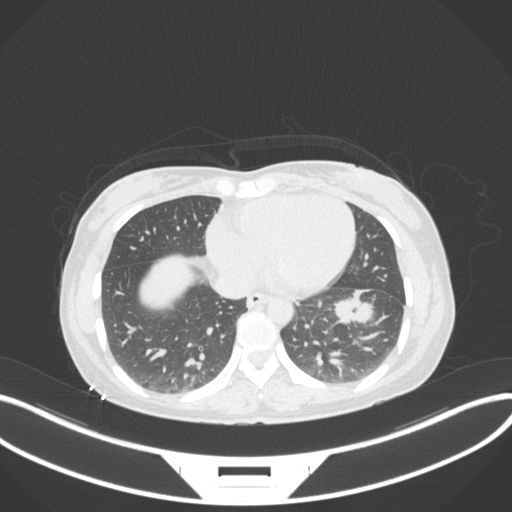
Chest CT, one axial slice. Position 121 of 361 along the scan axis. Reconstruction kernel B31f. 120 kVp. Lung window (W 1500 / L -600 HU). 512 × 512 image matrix, field of view 400 × 400 mm. Female patient, age 41 years. Case-level facts recorded for this patient, not image findings: clinical TNM (as recorded): T2a N3 M1b.
Annotated regions visible in this slice (rectangle marked by the reading radiologist):
- lung tumour (recorded histology: adenocarcinoma): bounding box <328,288,382,330> (left, top, right, bottom; pixels)